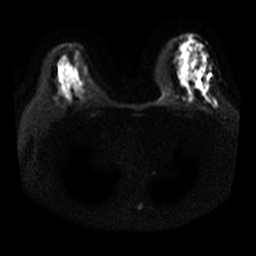
Breast MRI, one axial slice. Slice 18 of 29 in the series (ordered by position). Diffusion-weighted series; image 2 of 4 stored at this slice position (different b-values; order by instance number). 3 T. 5 mm slice thickness. 256 × 256 image matrix, field of view 340 × 340 mm. Female patient.
Structures marked on this image (manually delineated by an expert):
- tumour on diffusion-weighted imaging: bounding box [x1, y1, x2, y2] px = [197, 67, 206, 93]